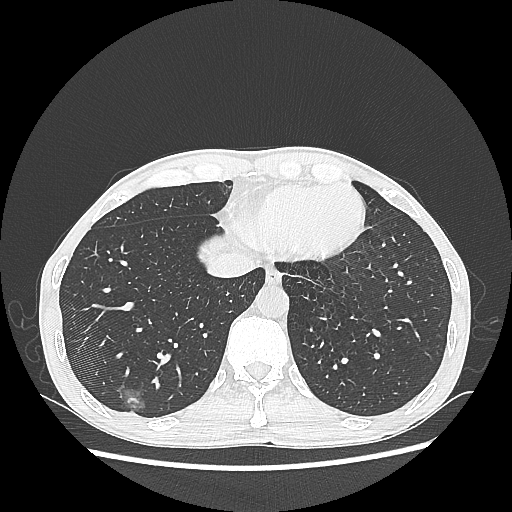
Chest CT, one axial slice; slice 72 of 270 in the series (ordered by position); reconstruction kernel LUNG; lung window (W 1500 / L -600 HU); 1.25 mm slice thickness; 512 × 512 image matrix, field of view 360 × 360 mm. Male patient, age 60 years. Case-level facts recorded for this patient, not image findings: clinical TNM (as recorded): T1c N0 M0.
Annotated regions visible in this slice (bounding box drawn by a radiologist):
- lung tumour (recorded histology: adenocarcinoma): bounding box [x1, y1, x2, y2] px = [114, 378, 145, 418]